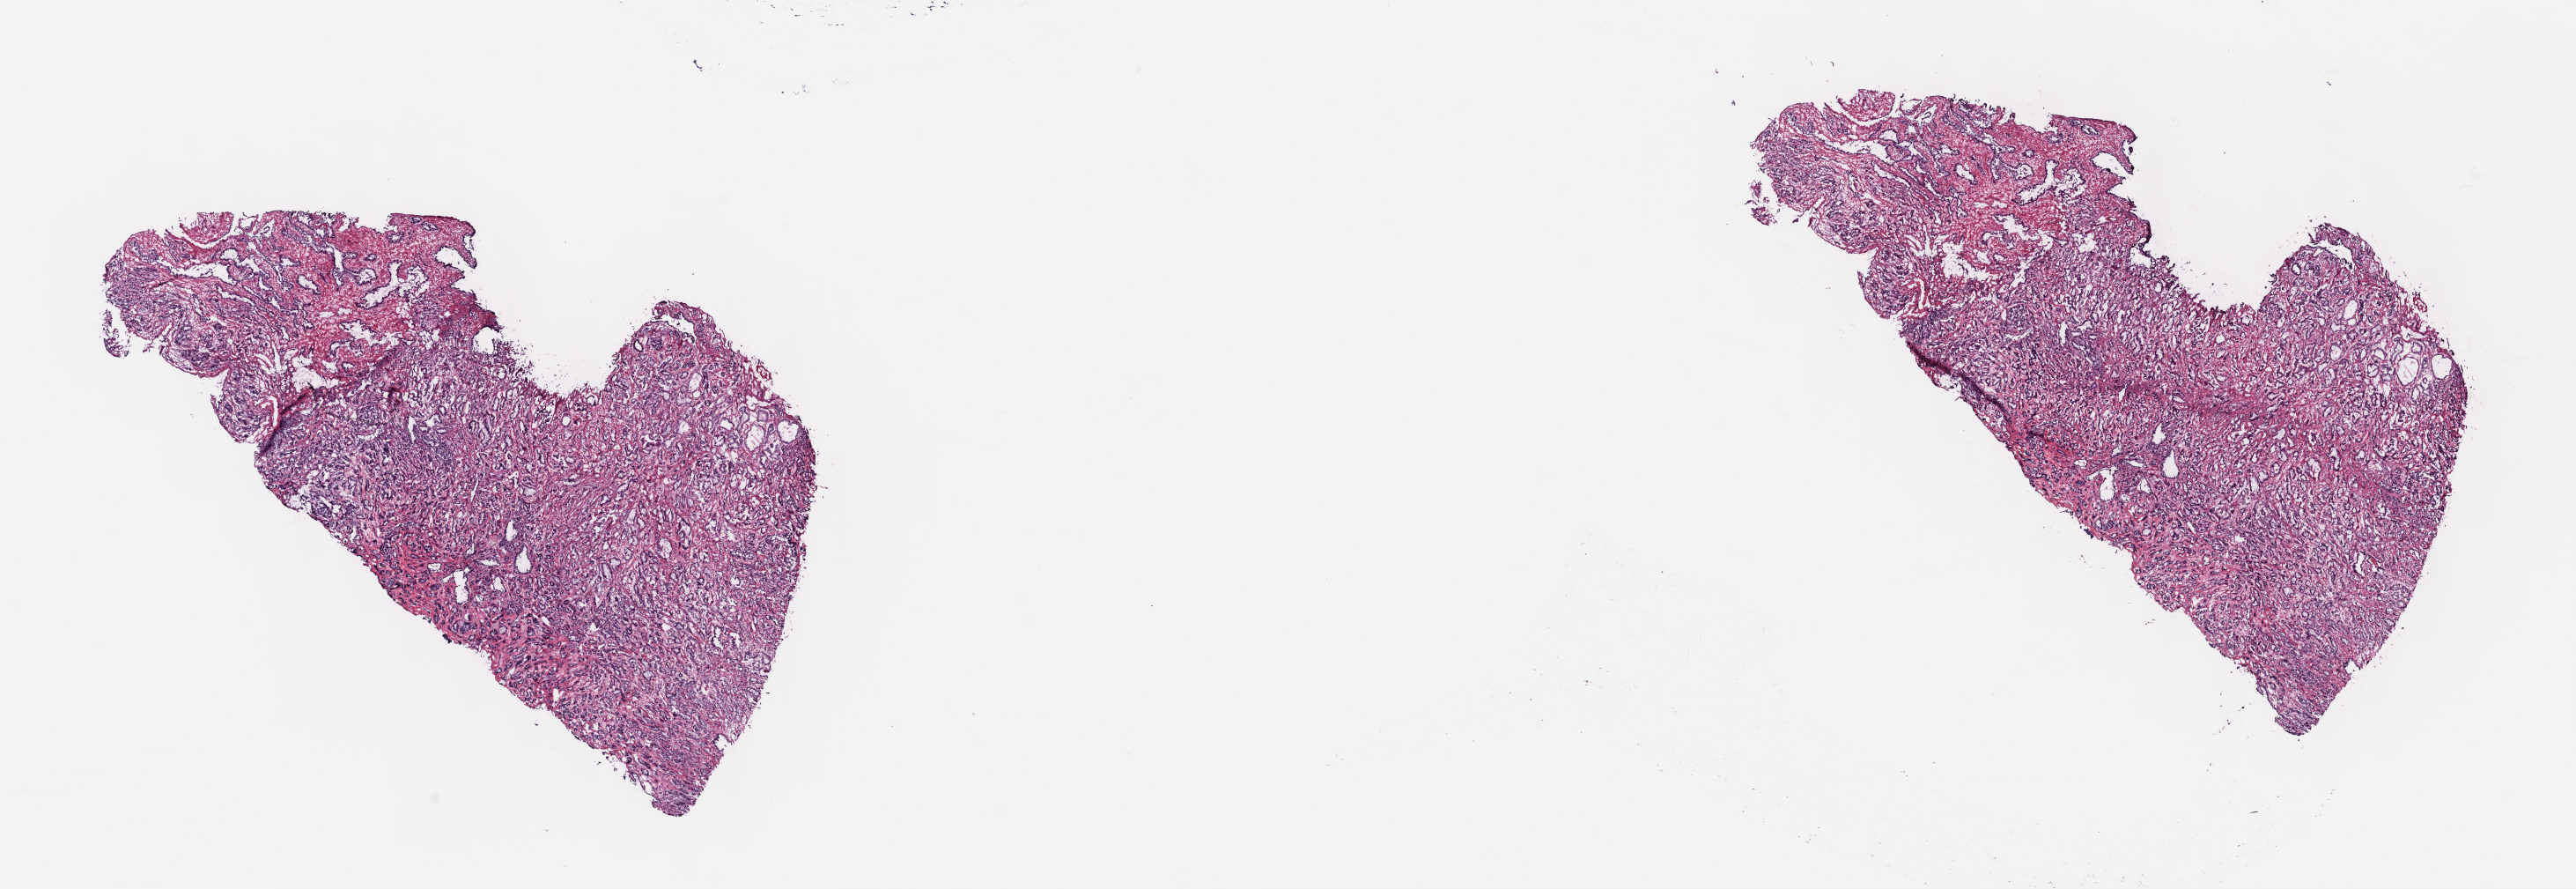
Whole-slide histology image, H&E-stained, a low-resolution overview of the entire scanned area, about 23.7 x 8.2 mm (acquisition: 40x scan); frozen section from the top of the tissue portion; primary tumour sample from the prostate. Male patient; age at initial diagnosis 57 years. Gleason score: 7 (3+4). Slide review estimates, as recorded: tumour cells 70%, tumour nuclei 75%, normal cells 10%, stromal cells 20%, necrosis 0%. Inflammatory infiltration, as recorded: lymphocyte infiltration 0%, monocyte infiltration 0%, neutrophil infiltration 0%.
Laterality: bilateral. Histologic diagnosis: Adenocarcinoma, NOS (prostate gland).